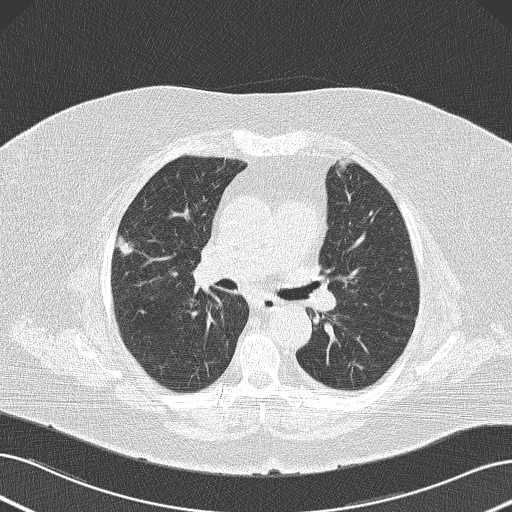
Low-dose screening chest CT, axial slice, first (baseline) screen, lung window (W 1500 / L -600 HU), 120 kVp, slice 66 of 145 in the series. Female, age 73 years at enrolment.
Lesion marked by an expert reader, box from (x=105, y=223) to (x=149, y=262) px. The exam's reader record, not a measurement of the box and not confirmed to be the same lesion: non-calcified nodule or mass ≥4 mm, right upper lobe, 15 × 11 mm, poorly defined margins, soft tissue attenuation. Official screen result: positive, change unspecified: nodule(s) >= 4 mm or enlarging nodule(s), mass(es), or other non-specific abnormalities suspicious for lung cancer. Lung cancer was diagnosed 55 days after this screen: neoplasm, malignant, right upper lobe, stage IA (AJCC 6th edition), 15 mm at pathology.